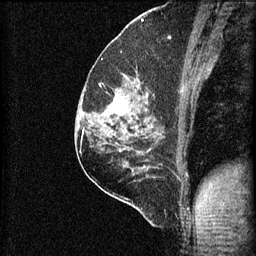
Breast MRI (dynamic contrast-enhanced), one sagittal slice. Position 37 of 60 along the scan axis. 3 images stored at this slice position (order not interpretable as contrast timing). 1.5 T. TE 4.2 ms, TR 8.2 ms. 256 × 256 image matrix, field of view 180 × 180 mm. Female patient, age 59 years.
Structures marked on this image (semi-automatically segmented with operator editing):
- analysis volume of interest (the breast-tissue region the enhancement analysis was run in; not a lesion): box from (x=92, y=74) to (x=155, y=131) px
- tumour enhancement mask (voxels above the 70 % enhancement threshold inside the analysis volume of interest): (x=106, y=94)–(x=149, y=115)